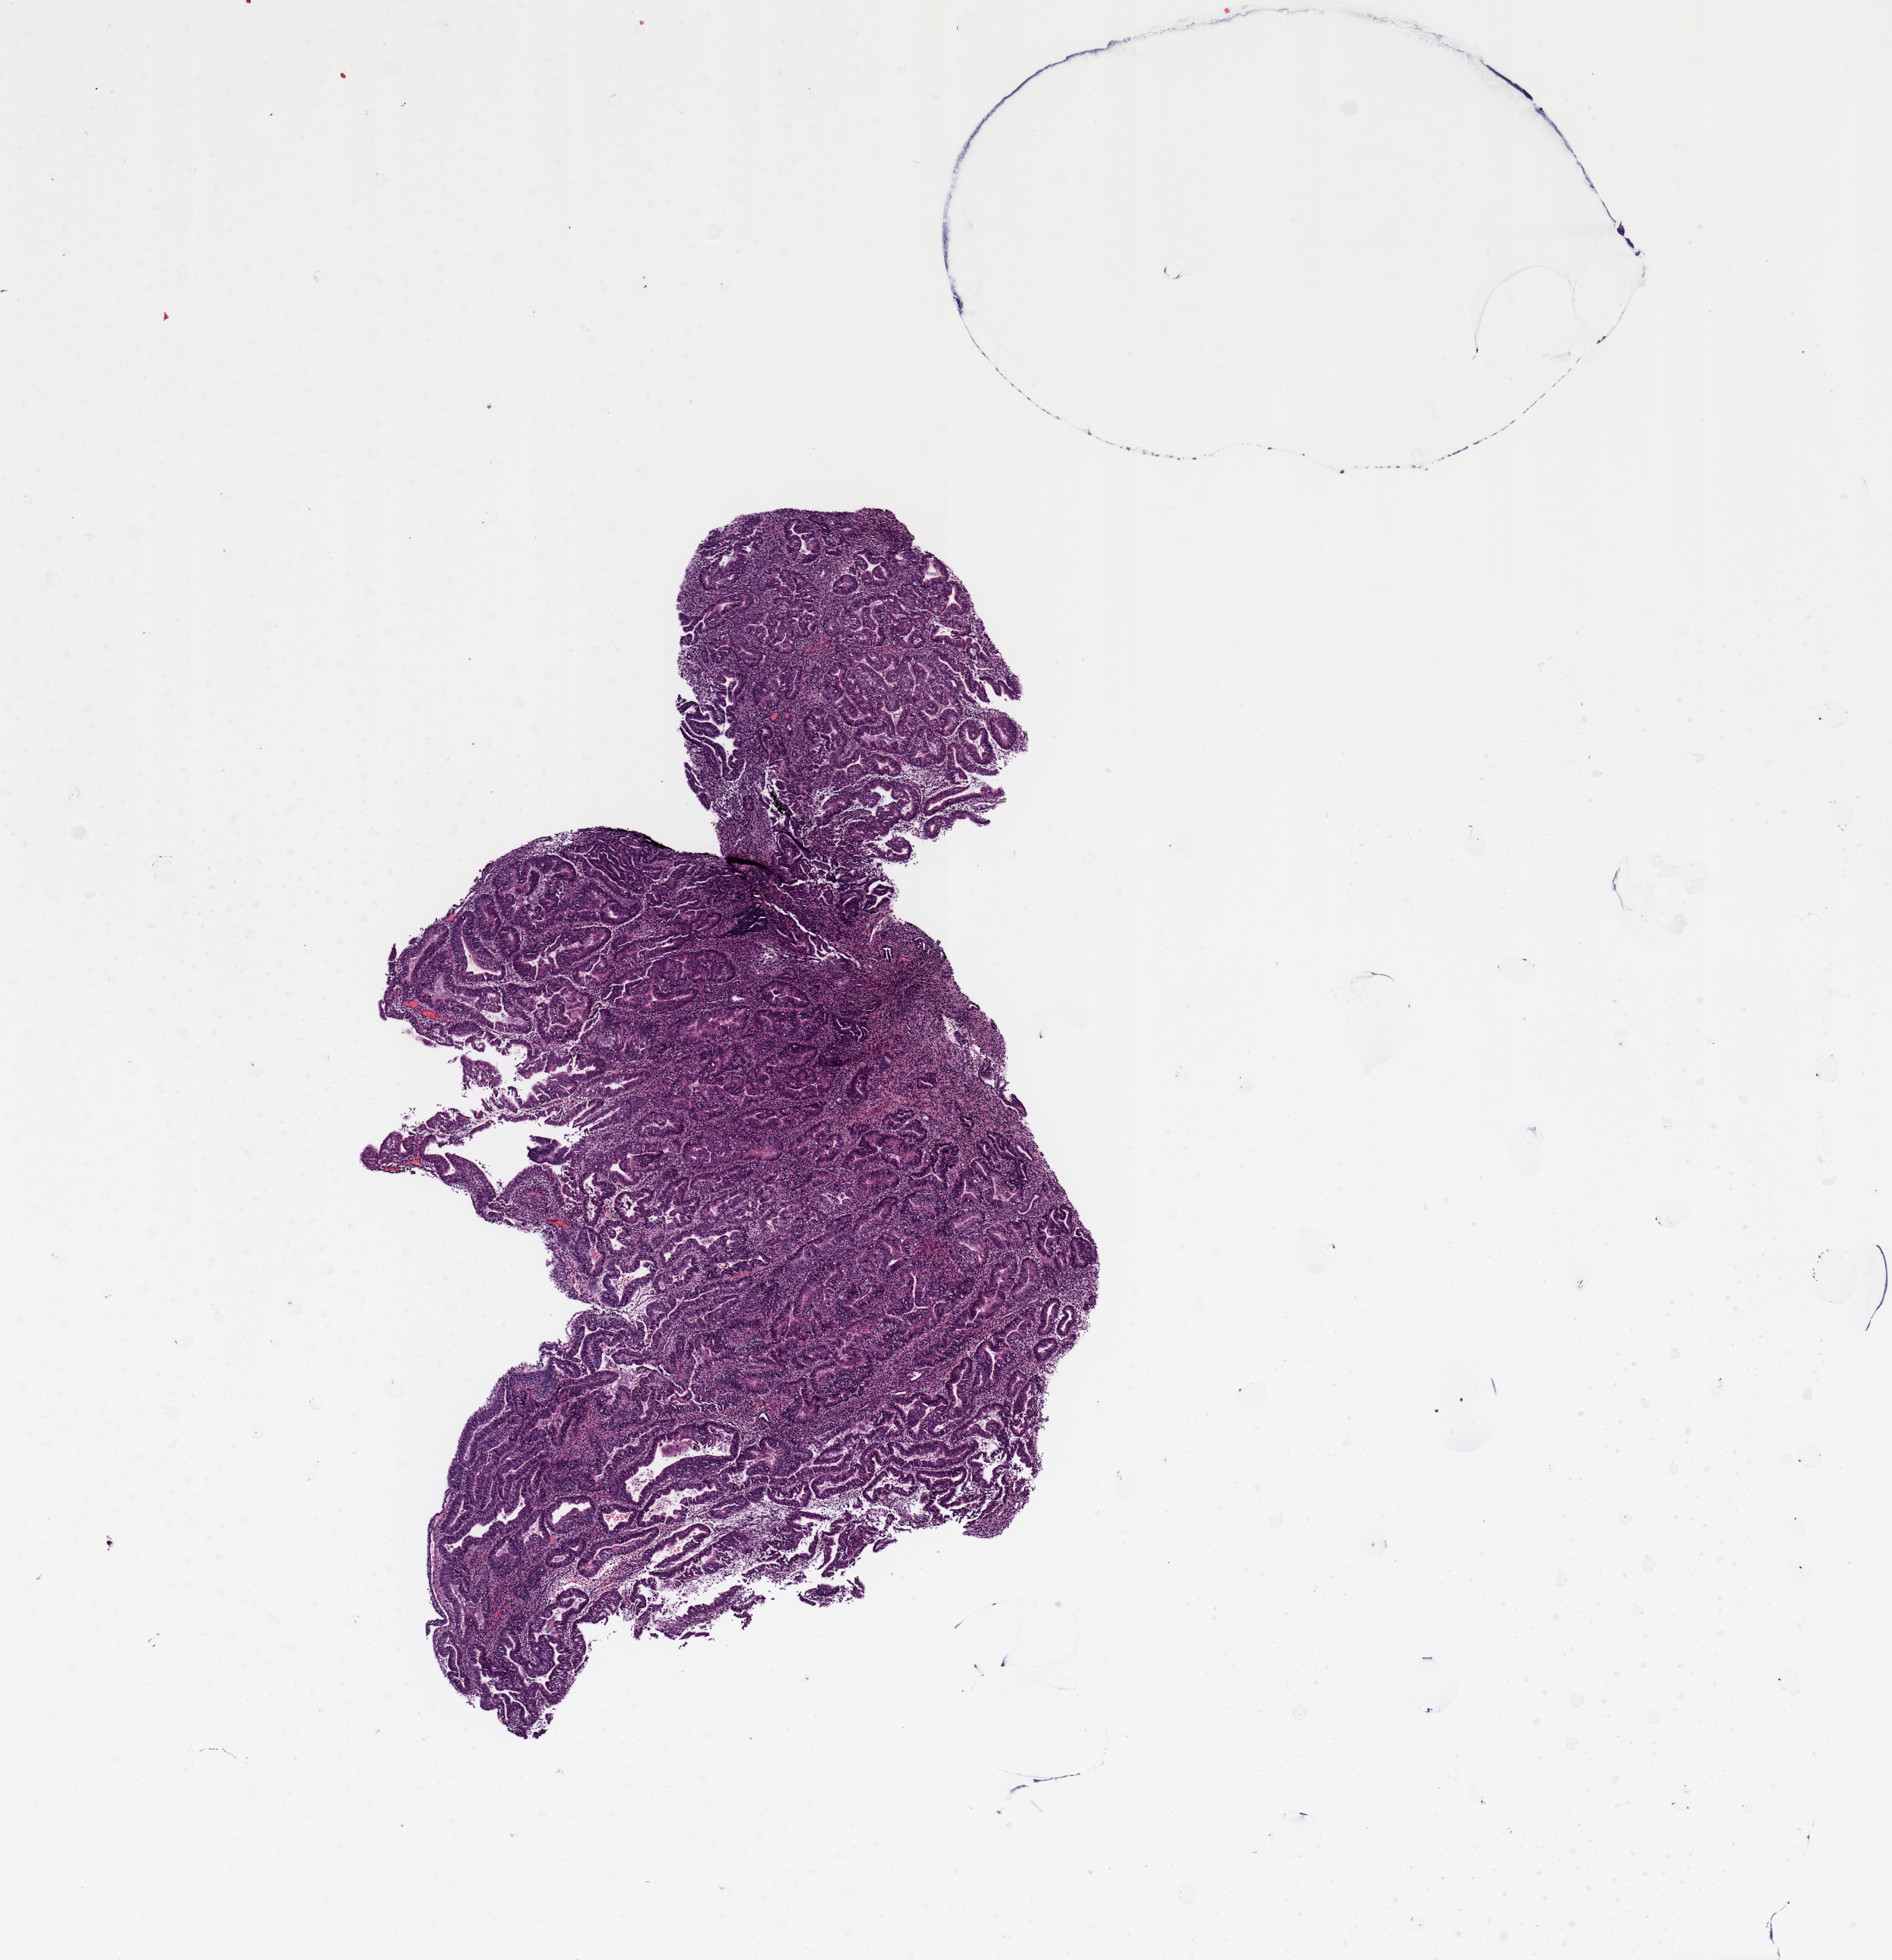
H&E-stained whole-slide image — low-resolution overview of the scanned area, about 9.8 x 10.2 mm, tumour tissue sample, sampled site: uterus. 37-year-old female patient.
Diagnosis: Endometrioid adenocarcinoma, NOS.